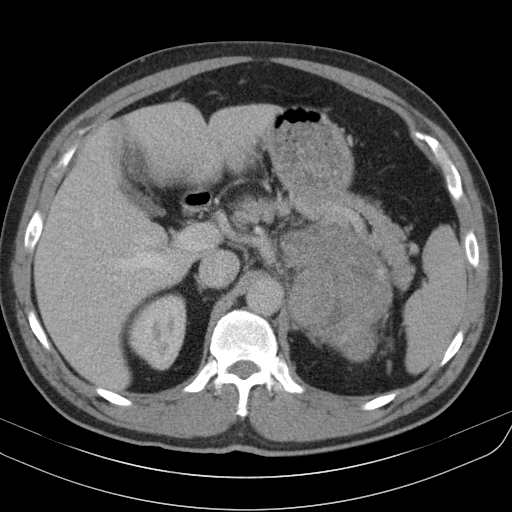
Contrast-enhanced abdominal CT, one axial slice. Position 70 of 91 along the scan axis. Reconstruction kernel B31s. 130 kVp. Intravenous contrast given. Soft-tissue window (W 400 / L 40 HU). 5 mm slice thickness. 512 × 512 image matrix, field of view 370 × 370 mm. Patient: male, 51 years. From the clinical record (not read from this slice): diagnosis: adrenocortical carcinoma; tumour side: left adrenal; tumour size at pathology: 18 cm; Ki-67 index: 40 %; stage (as recorded): 3.
Annotated regions visible in this slice (semi-automatic segmentation, software-assisted and operator-edited):
- mass: bounding box <280,222,390,359> (left, top, right, bottom; pixels)